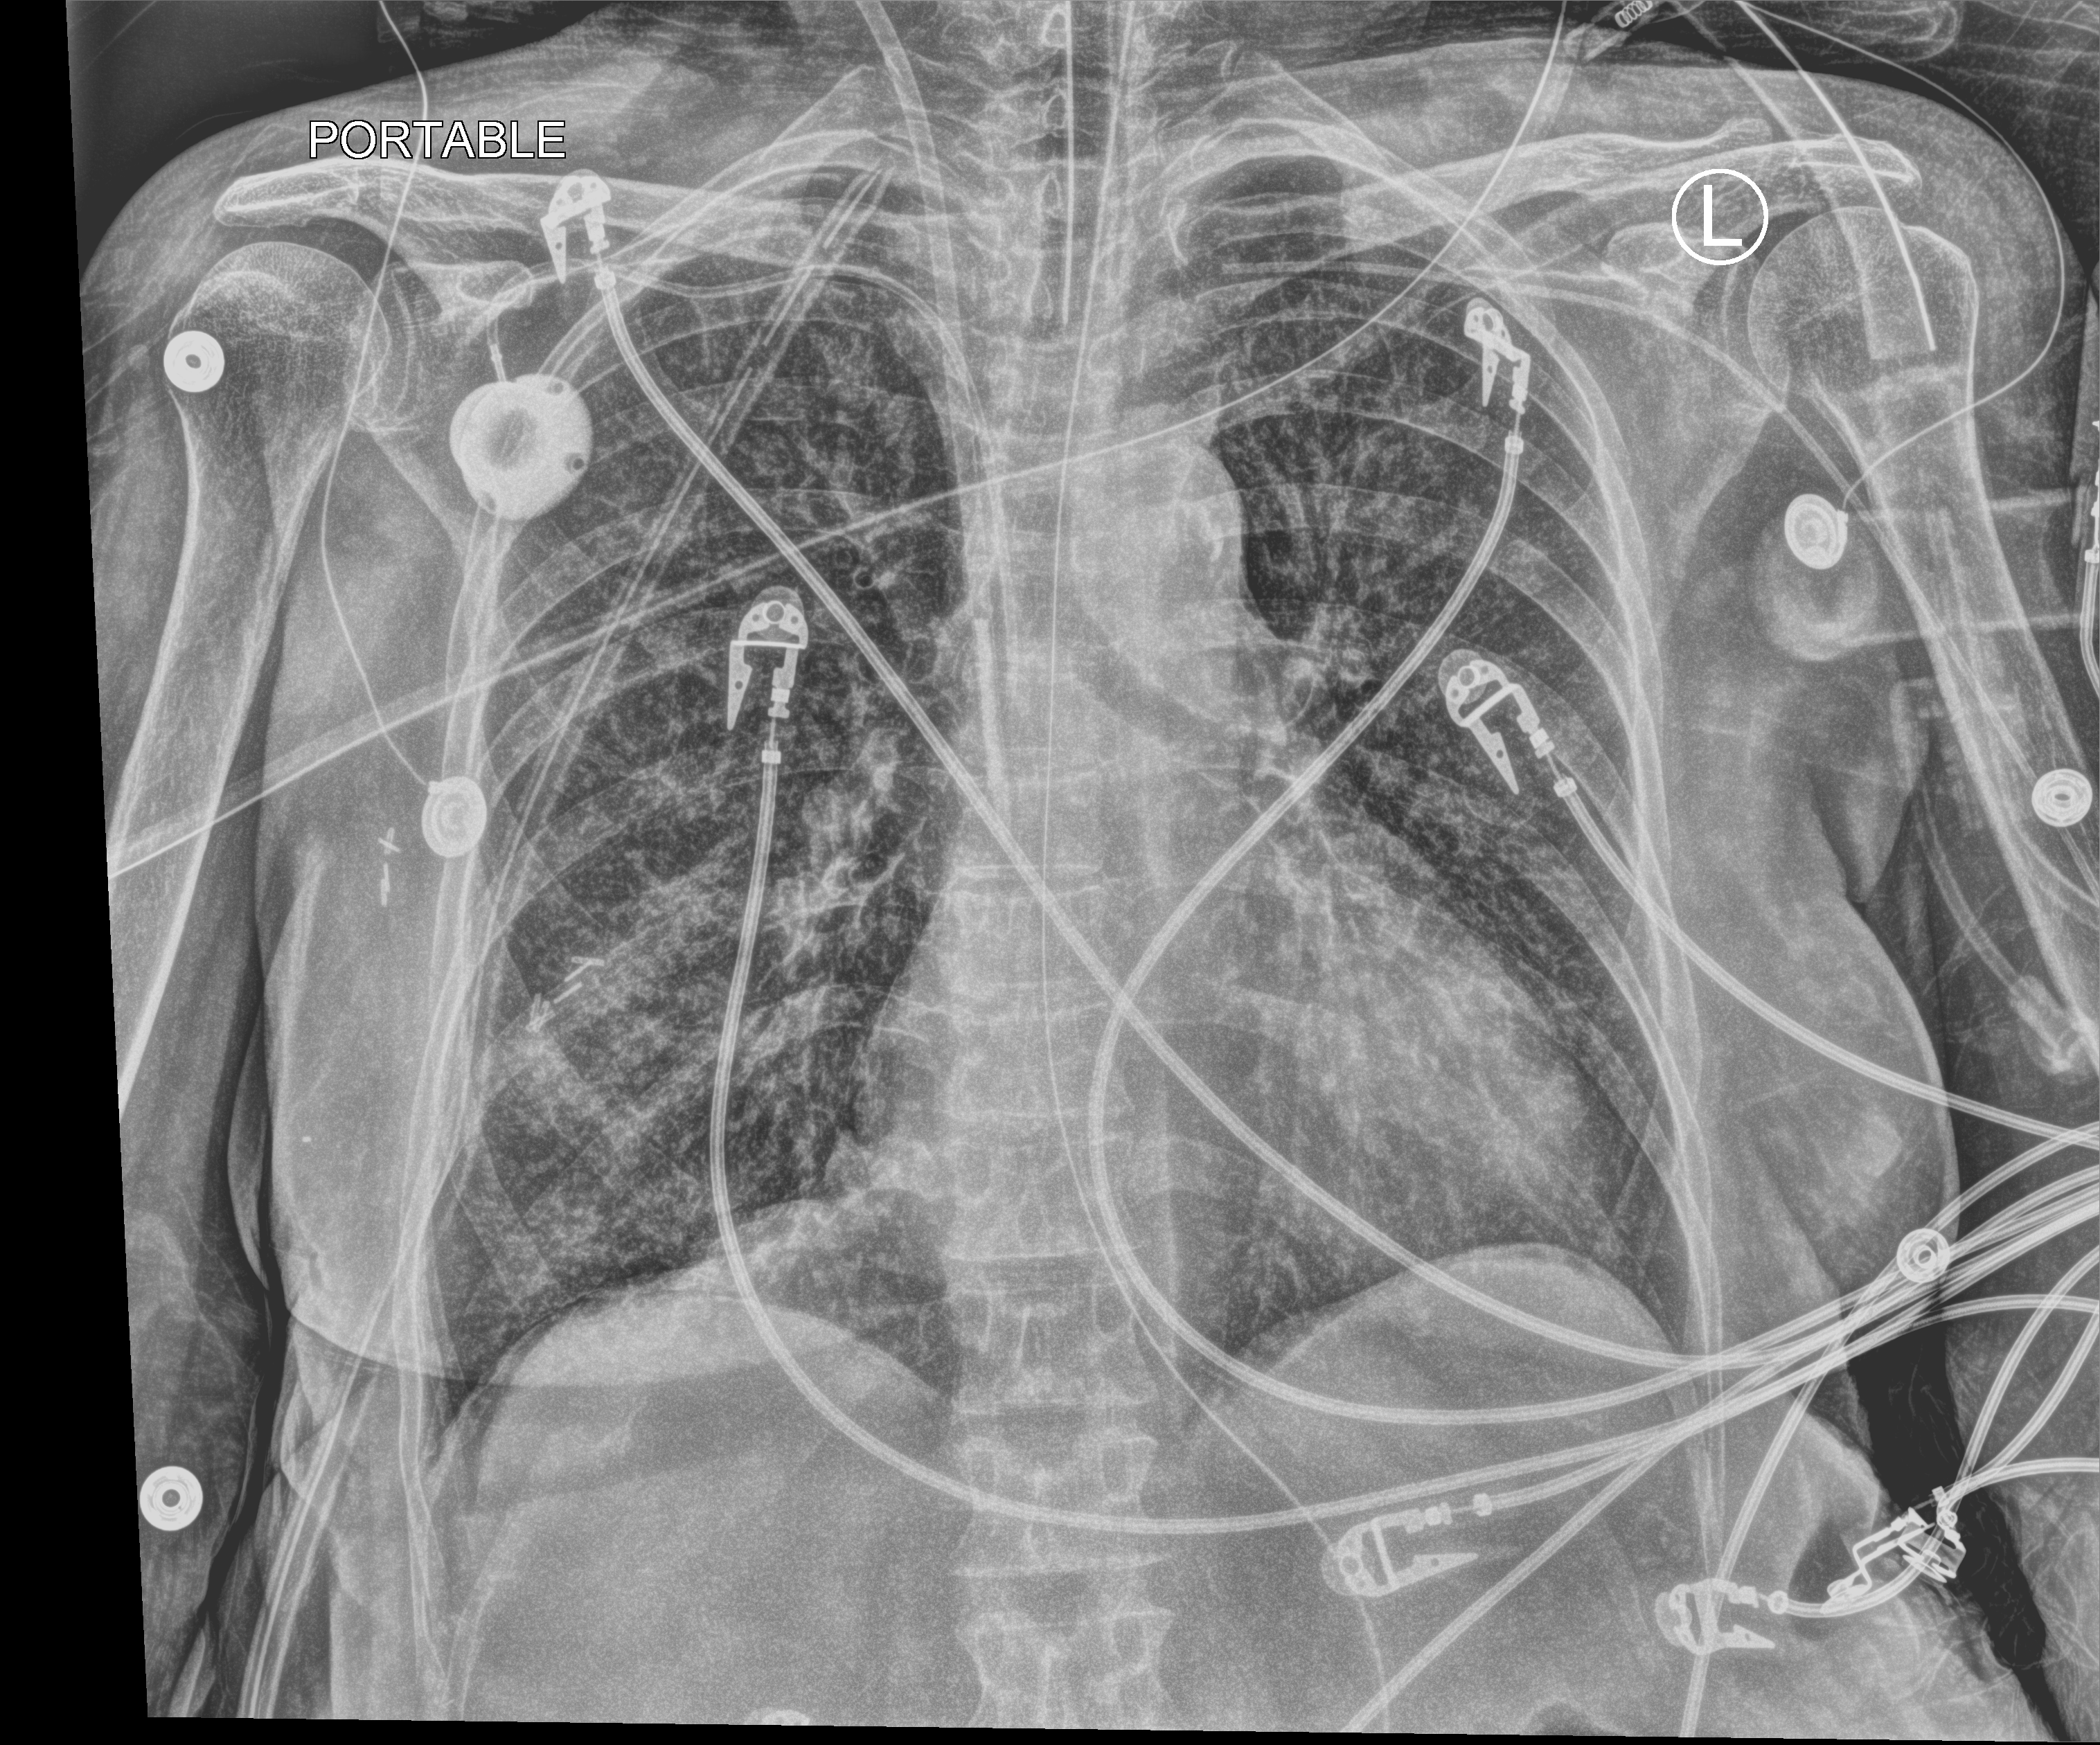
Bedside chest radiograph (computed radiography). Female patient hospitalised with COVID-19, age 60–74 years.
From the hospital-stay record, not from the radiograph (when in the stay this image was taken is not recorded):
- admitted to intensive care during this hospital stay: yes
- chronic kidney disease (admission record): no
- smoking status (admission record): former